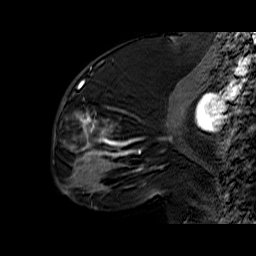
Breast MRI (dynamic contrast-enhanced), one sagittal slice. Position 24 of 60 along the scan axis. Dynamic contrast-enhanced series, time point 2 of 6 at this slice position (early post-contrast). 1.5 T. TE 6.4 ms, TR 32.9 ms. 4 mm slice thickness. 256 × 256 image matrix, field of view 200 × 200 mm. Female patient. Case-level facts recorded for this patient, not image findings: setting: breast cancer imaged before/during neoadjuvant chemotherapy; receptor status: triple-negative.
Outlined on this slice (semi-automatic segmentation, software-assisted and operator-edited):
- analysis volume of interest (the breast-tissue region the enhancement analysis was run in; not a lesion): bounding box <55,65,159,174> (left, top, right, bottom; pixels)
- tumour enhancement mask (voxels above the 100 % enhancement threshold inside the analysis volume of interest): <69,81,159,172>